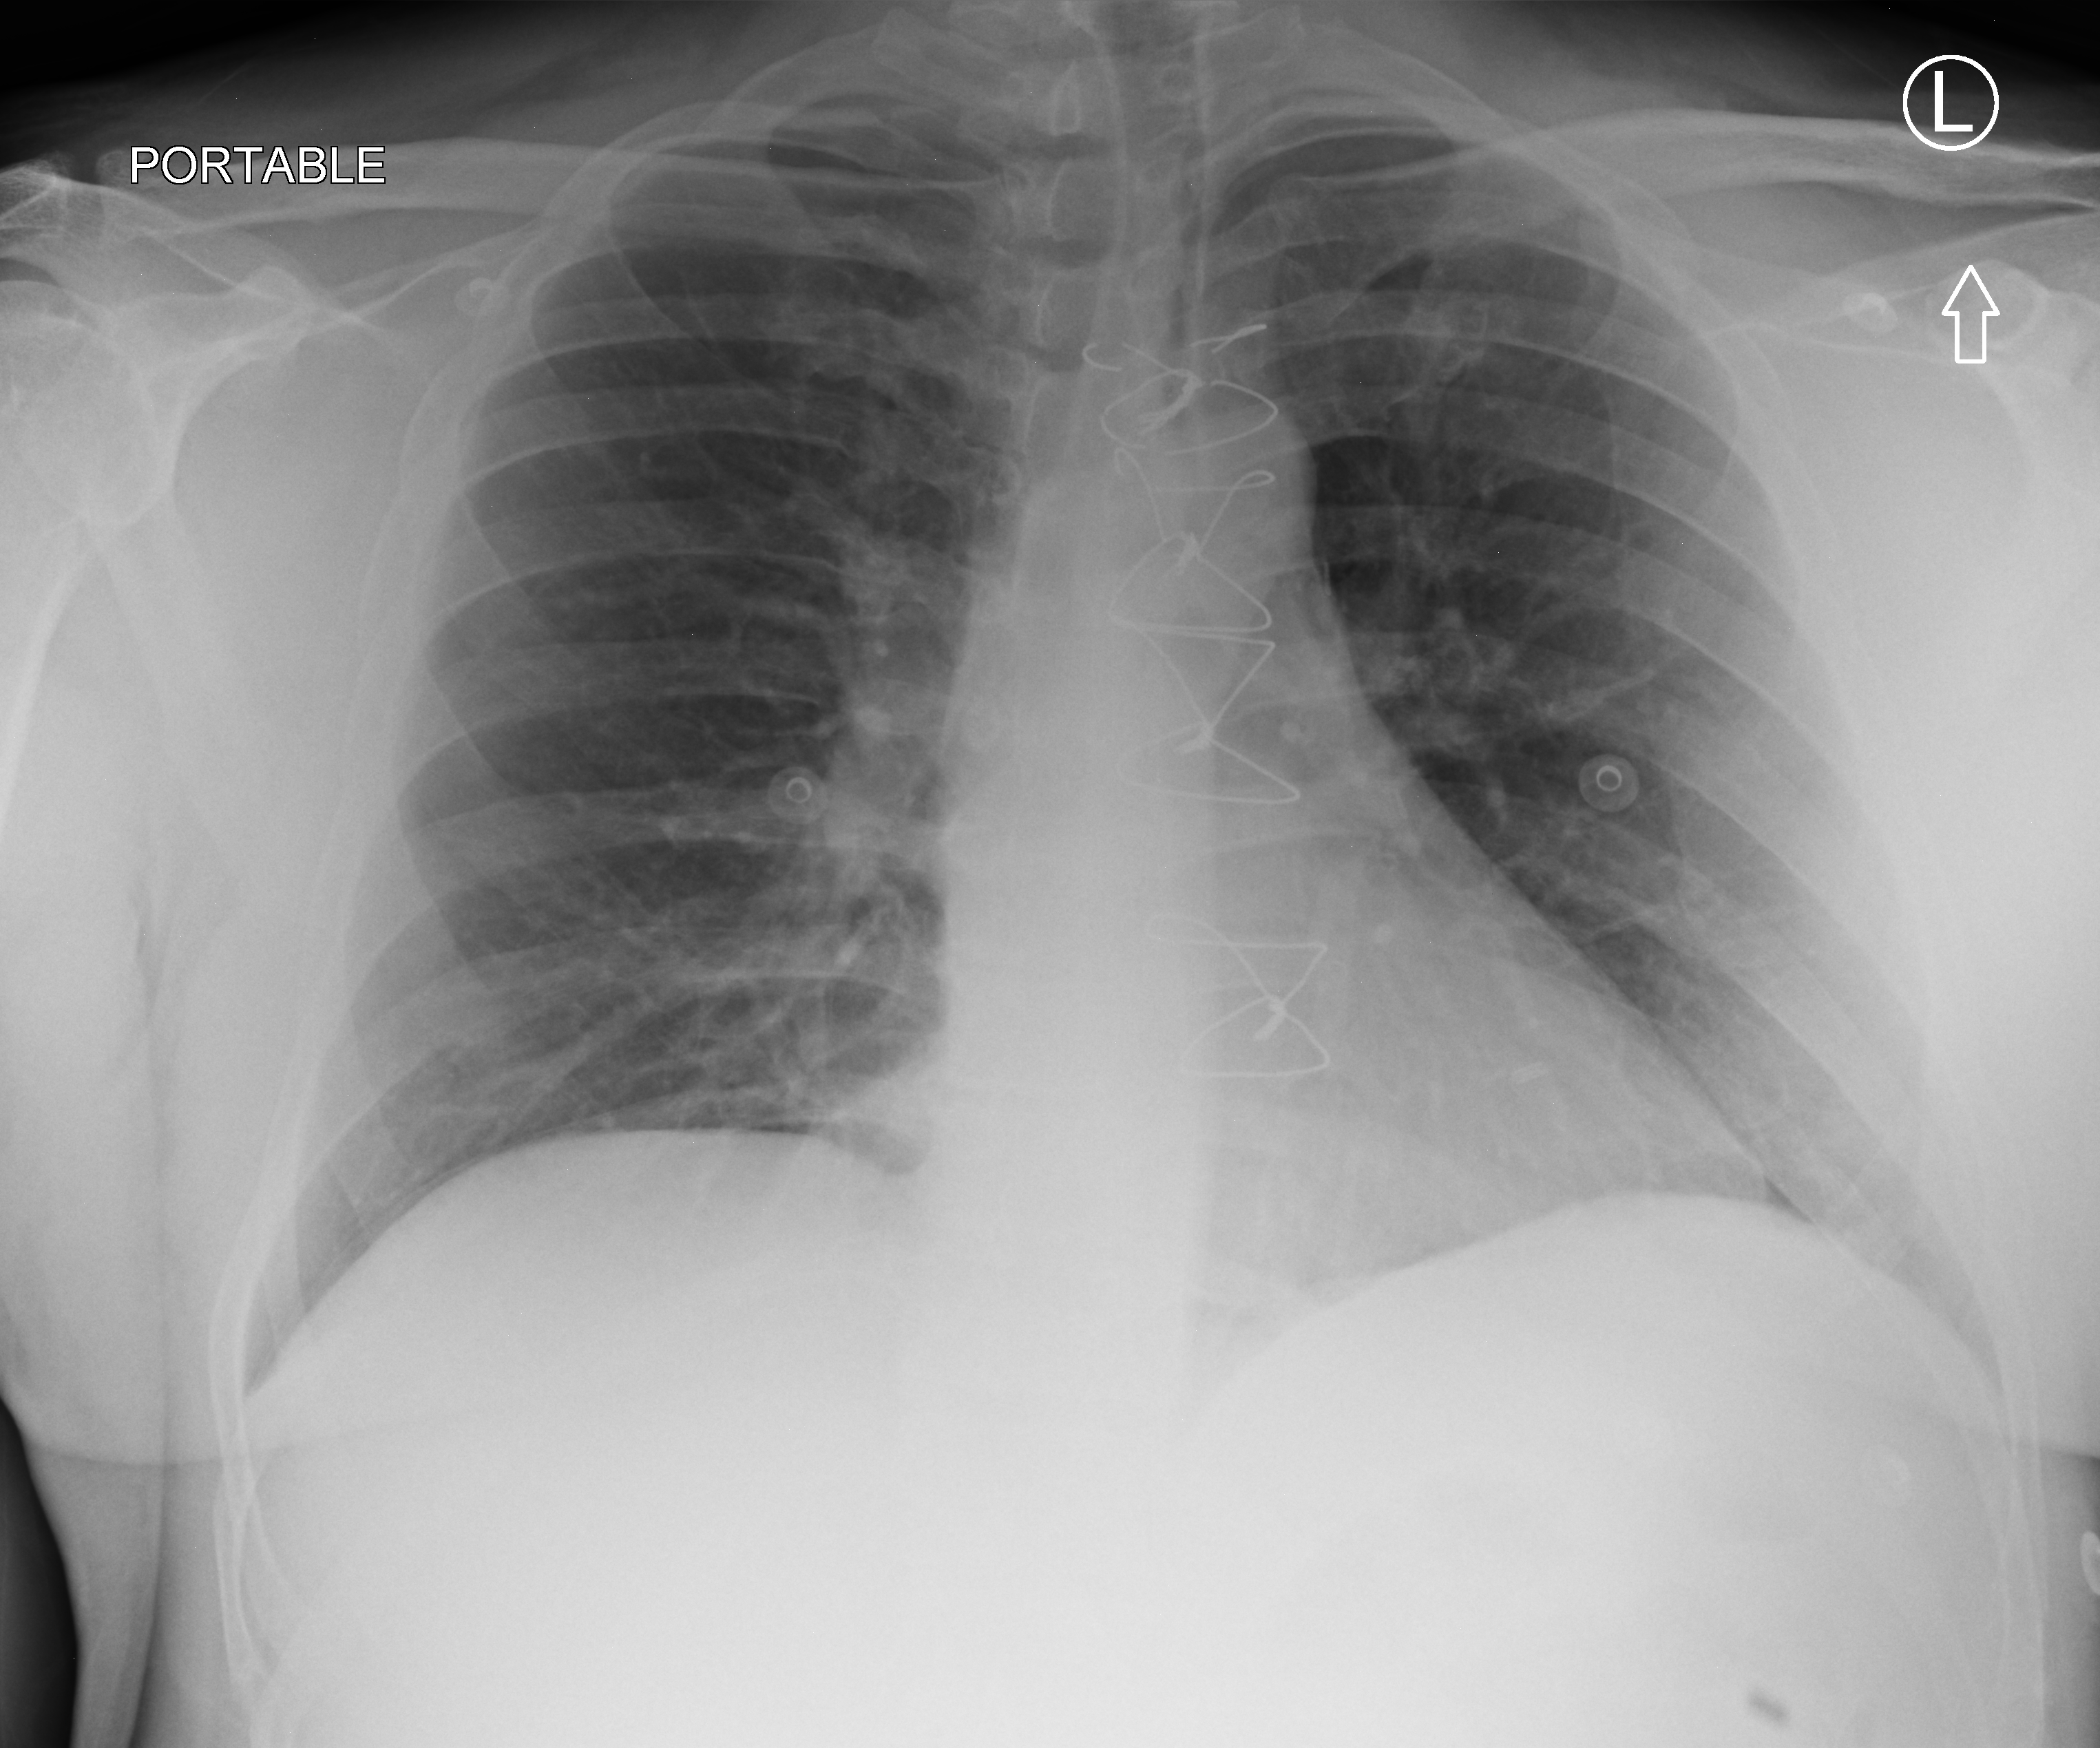
Portable chest radiograph. Male patient hospitalised with COVID-19, age 18–59 years.
From the hospital-stay record, not from the radiograph (when in the stay this image was taken is not recorded): COPD (admission record): no; mechanically ventilated during this hospital stay: no.